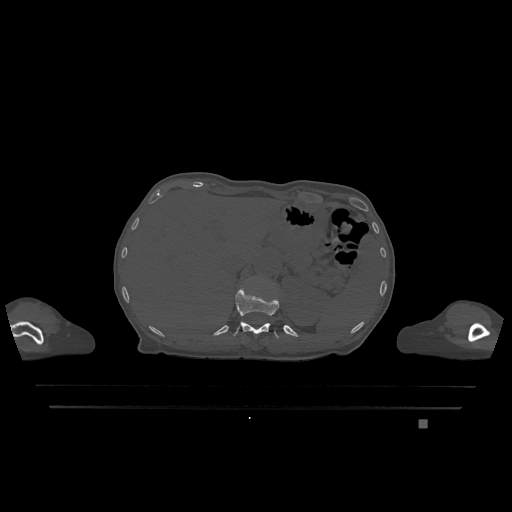
CT including the spine, one axial slice. Position 528 of 1317 along the scan axis. Bone window (W 1800 / L 400 HU). 0.5 mm slice thickness. 512 × 512 image matrix, field of view 500 × 500 mm. Female patient, age 74 years. Case-level facts recorded for this patient, not image findings: primary cancer: lung; vertebrae with lytic lesions (as recorded): T1, T4, T5, T6, L4, L5.
Outlined on this slice (semi-automatically segmented with operator editing):
- T12 vertebra: bounding box <233,286,279,339> (left, top, right, bottom; pixels)